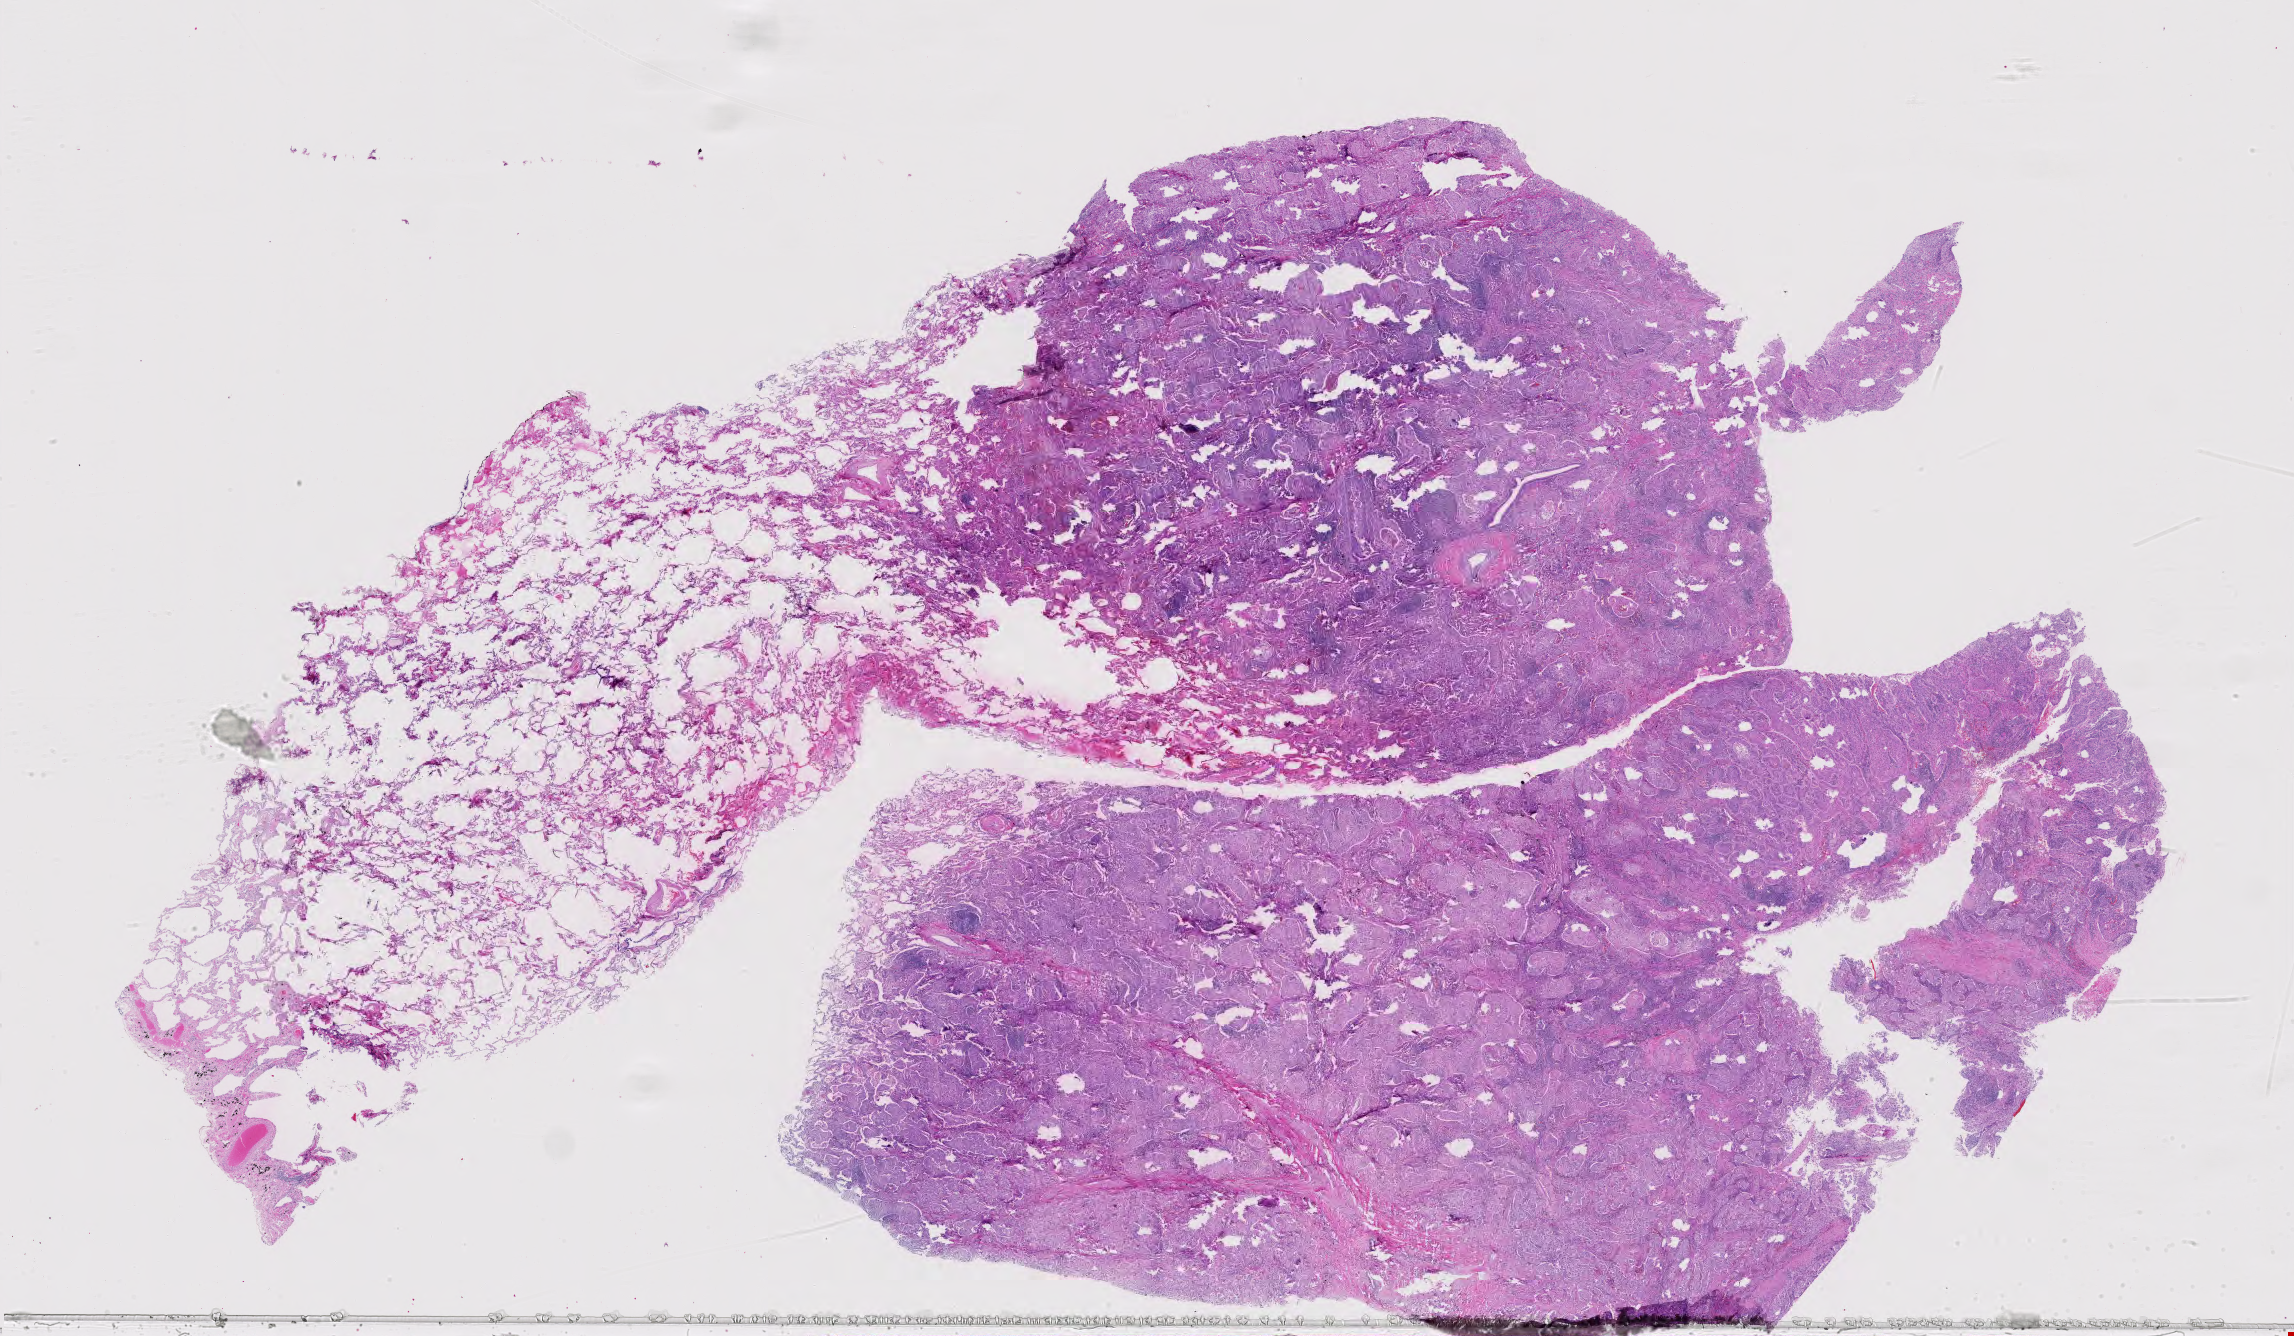
Whole-slide histology image, H&E — whole scanned area (about 33.3 x 19.4 mm, slide scanned at 40x) shown as a low-resolution overview, formalin-fixed paraffin-embedded (FFPE) diagnostic section, primary tumour sample from the lung. Male, age 73 years at initial diagnosis.
AJCC pathologic stage: IIA (7th edition). Pathologic diagnosis: Squamous cell carcinoma, NOS (lower lobe, lung).